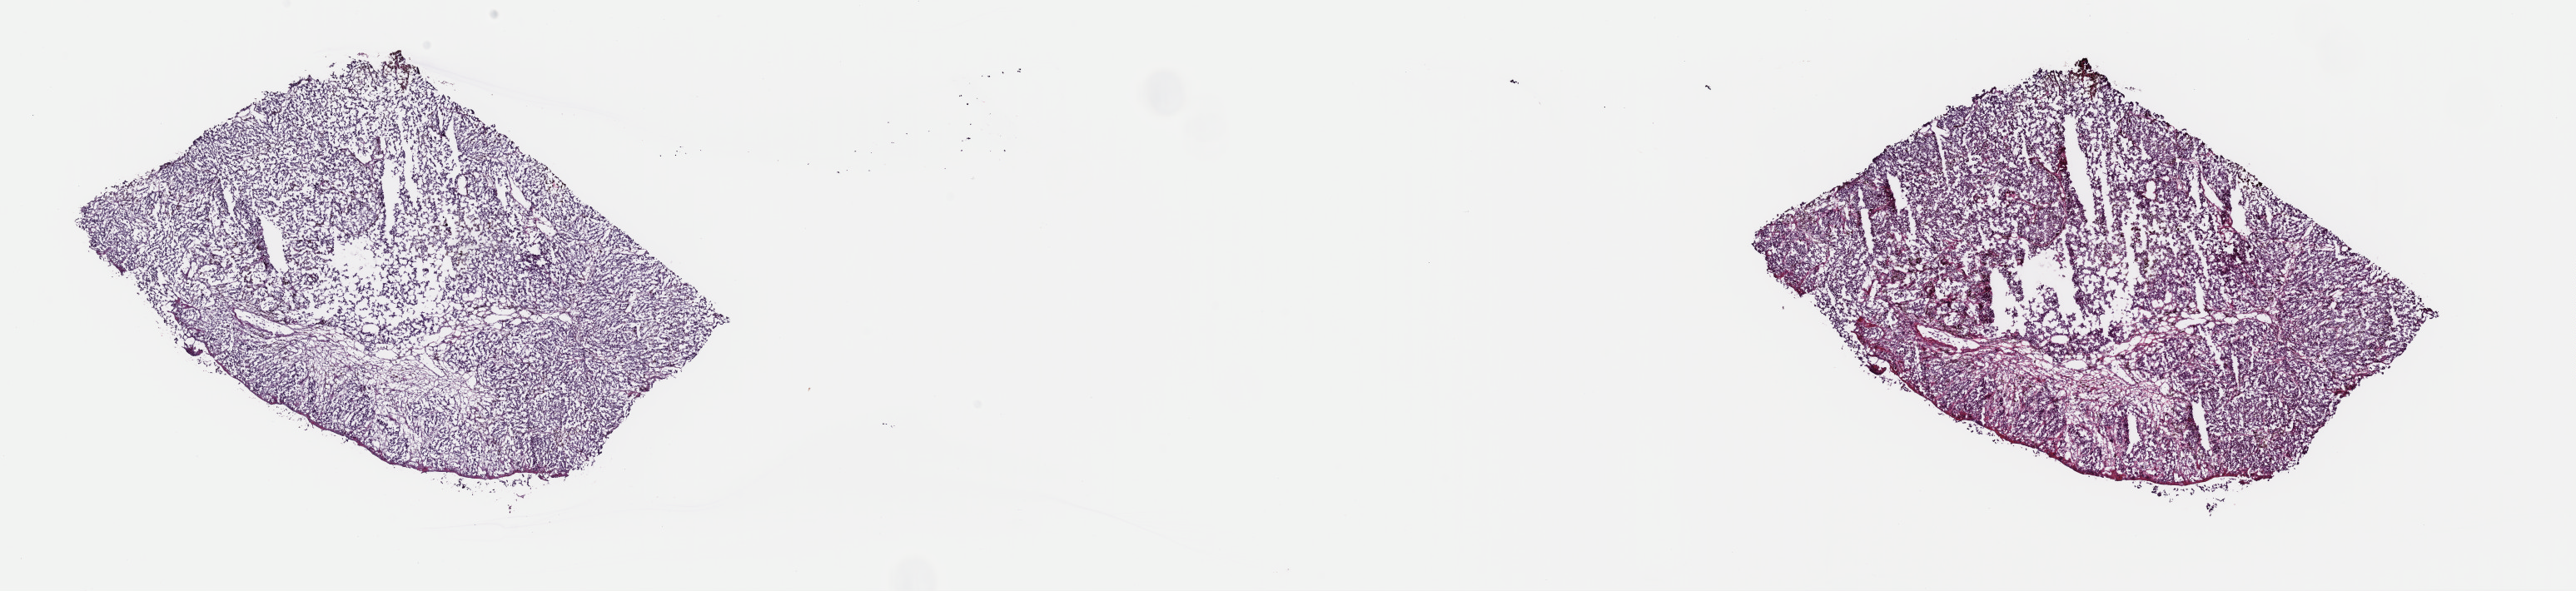
Hematoxylin and eosin (H&E) stained whole-slide image — a low-resolution overview of the entire scanned area, about 24.4 x 5.6 mm. Frozen section from the top of the tissue portion. Sample: primary tumour, skin. Male, age 61 years at initial diagnosis. Composition of this section per pathologist review: tumour cells 90%, tumour nuclei 85%, normal cells 0%, stromal cells 0%, necrosis 10%. Infiltration values recorded for this section: lymphocyte infiltration 3%, monocyte infiltration 4%, neutrophil infiltration 0%.
Diagnosis: Nodular melanoma.